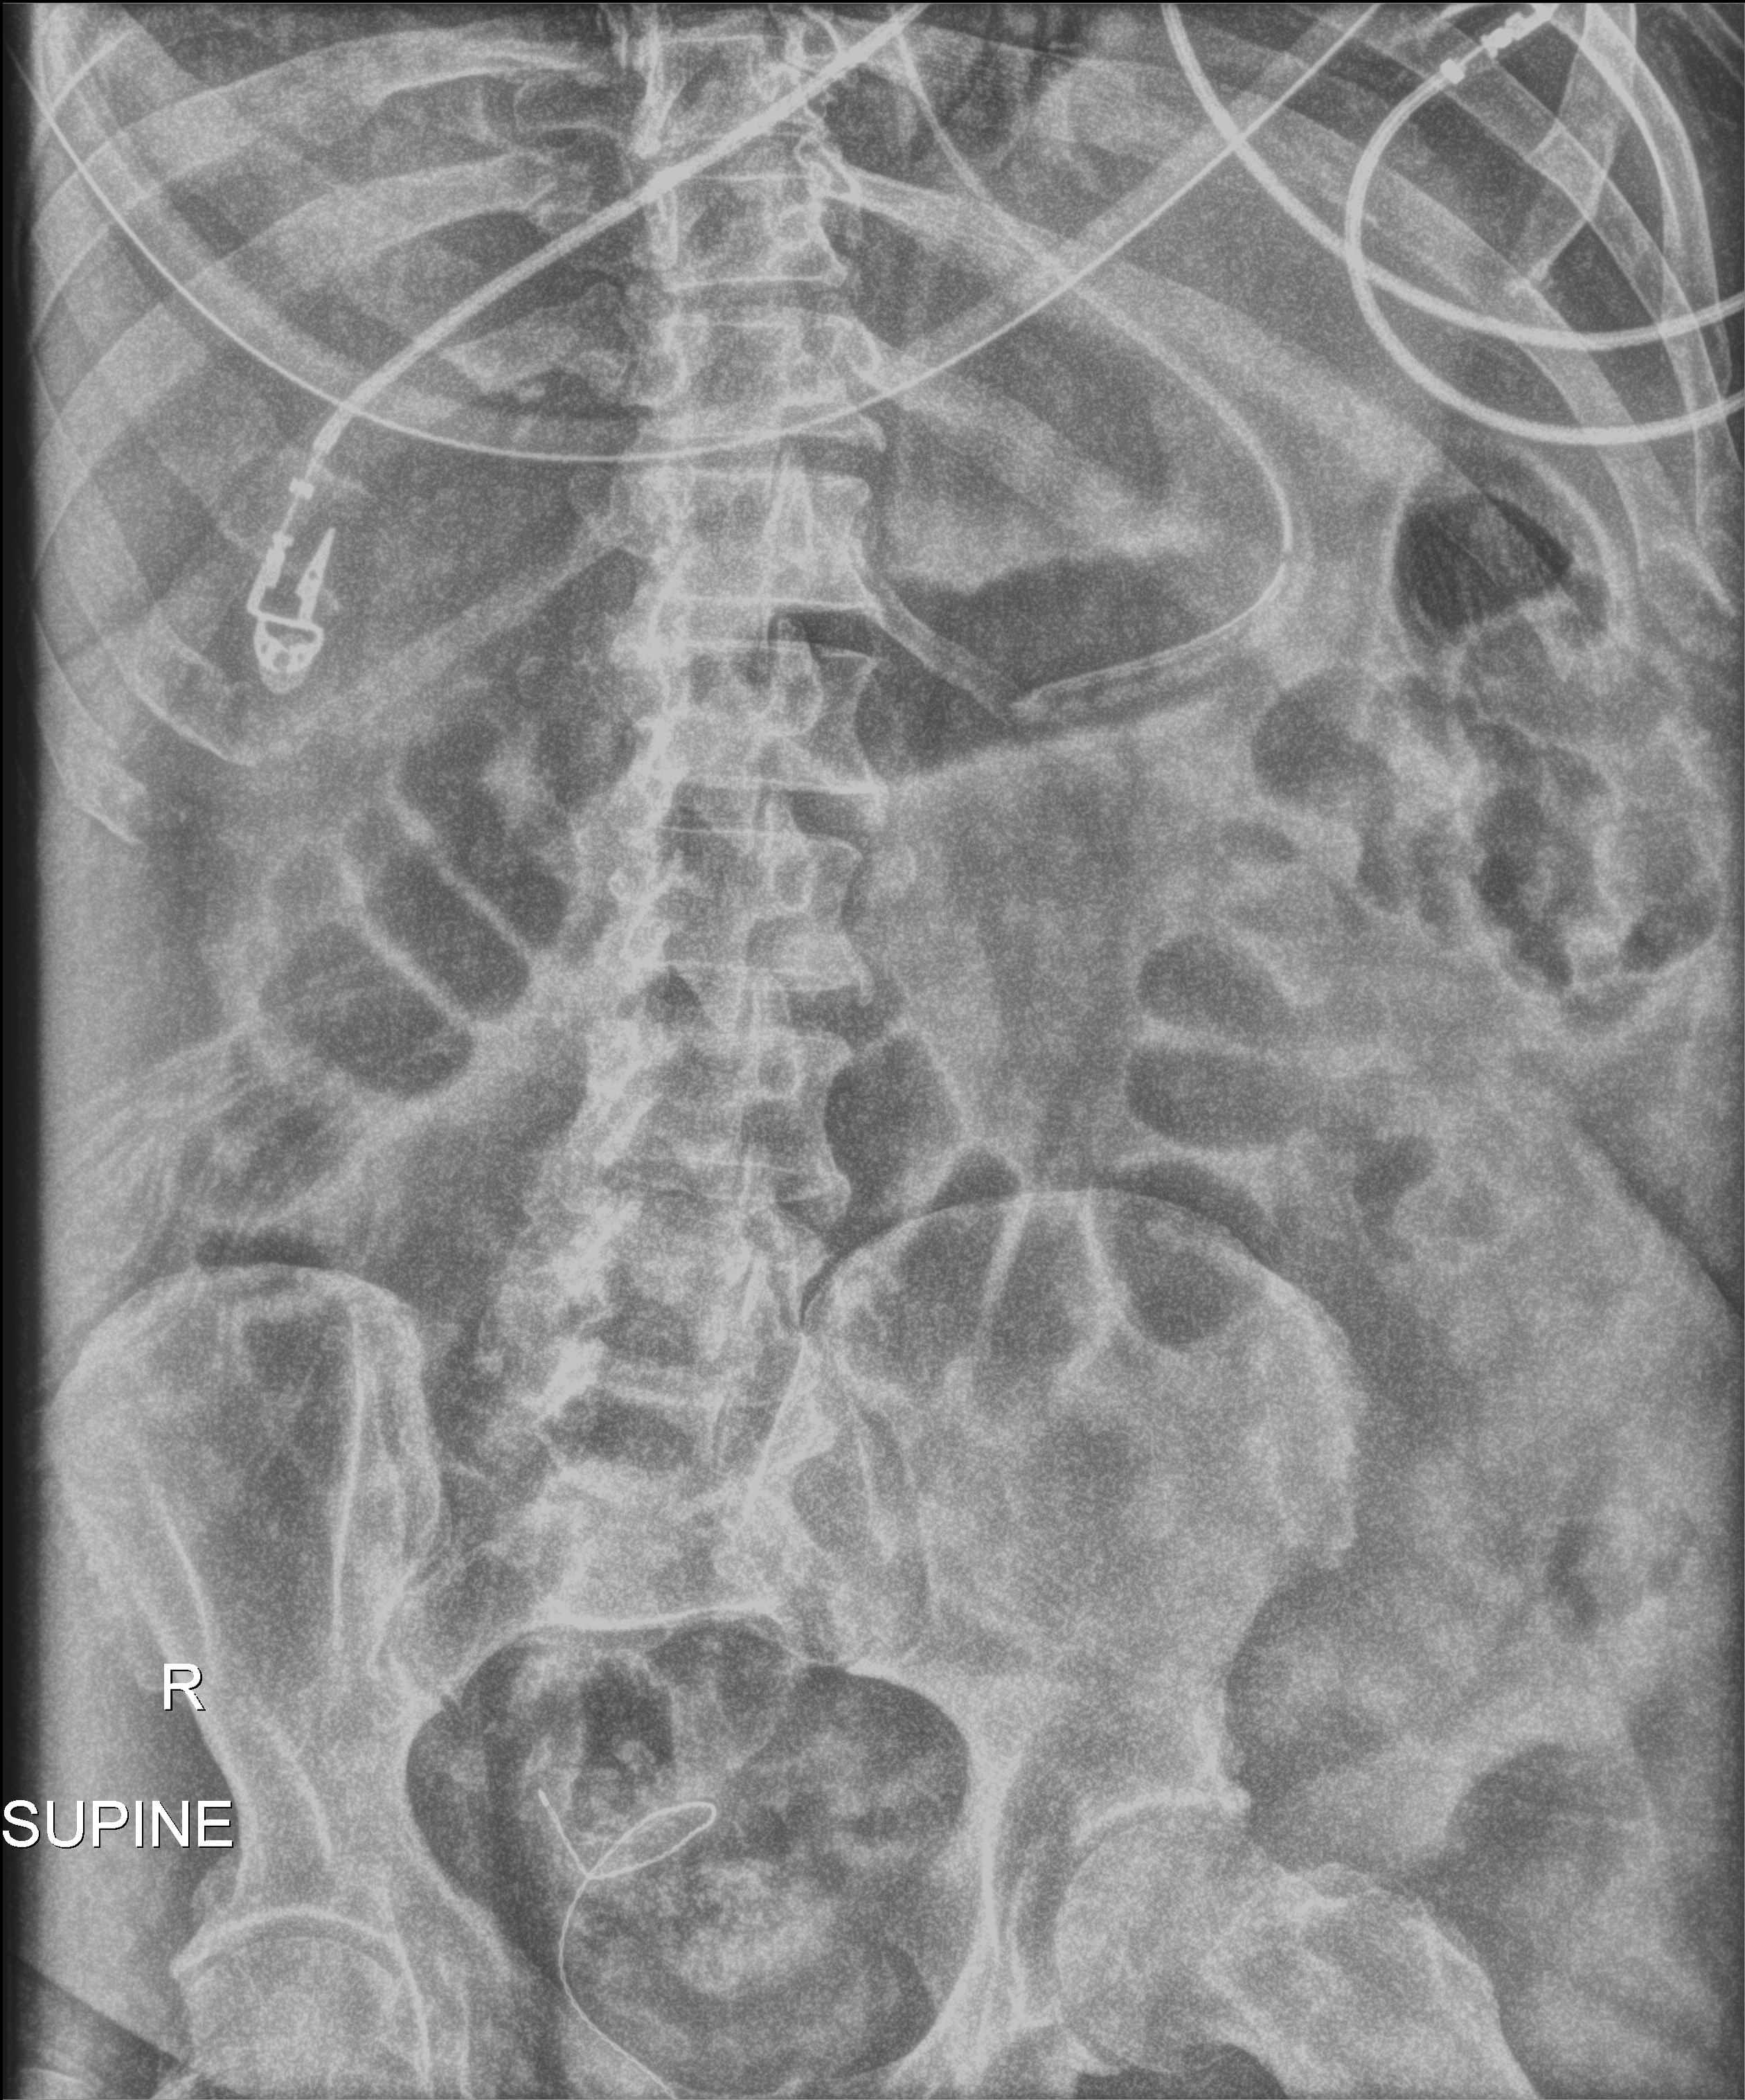
Abdomen X-ray (portable); anteroposterior (AP) projection. Patient hospitalised with COVID-19; male, aged 18–59 years.
From the hospital-stay record, not from the radiograph (when in the stay this image was taken is not recorded): mechanically ventilated during this hospital stay: yes; admitted to intensive care during this hospital stay: yes; diabetes (admission record): no.